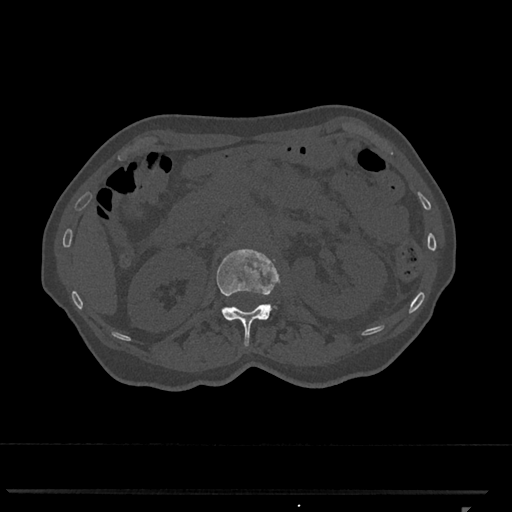
CT including the spine, one axial slice; position 396 of 793 along the scan axis; reconstruction kernel Br40s/3; bone window (W 1800 / L 400 HU); 0.5 mm slice thickness; 512 × 512 image matrix, field of view 380 × 380 mm. Female patient, age 62 years. From the clinical record (not read from this slice): primary cancer: renal.
Structures marked on this image (semi-automatically segmented with operator editing):
- L1 vertebra: box from (x=217, y=249) to (x=281, y=347) px